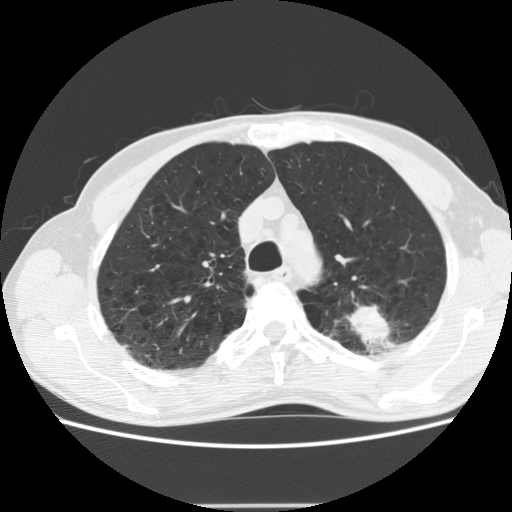
Low-dose screening chest CT, one axial slice. Slice 147 of 191 in the series (ordered by position). 120 kVp. Lung window (W 1500 / L -600 HU). 512 × 512 image matrix, field of view 352 × 352 mm.
Structures marked on this image (outlined manually by an expert reader):
- lesion 1 (tumor, upper lobe of left lung): bounding box (x1, y1, x2, y2) in pixels: (349, 305, 390, 343)